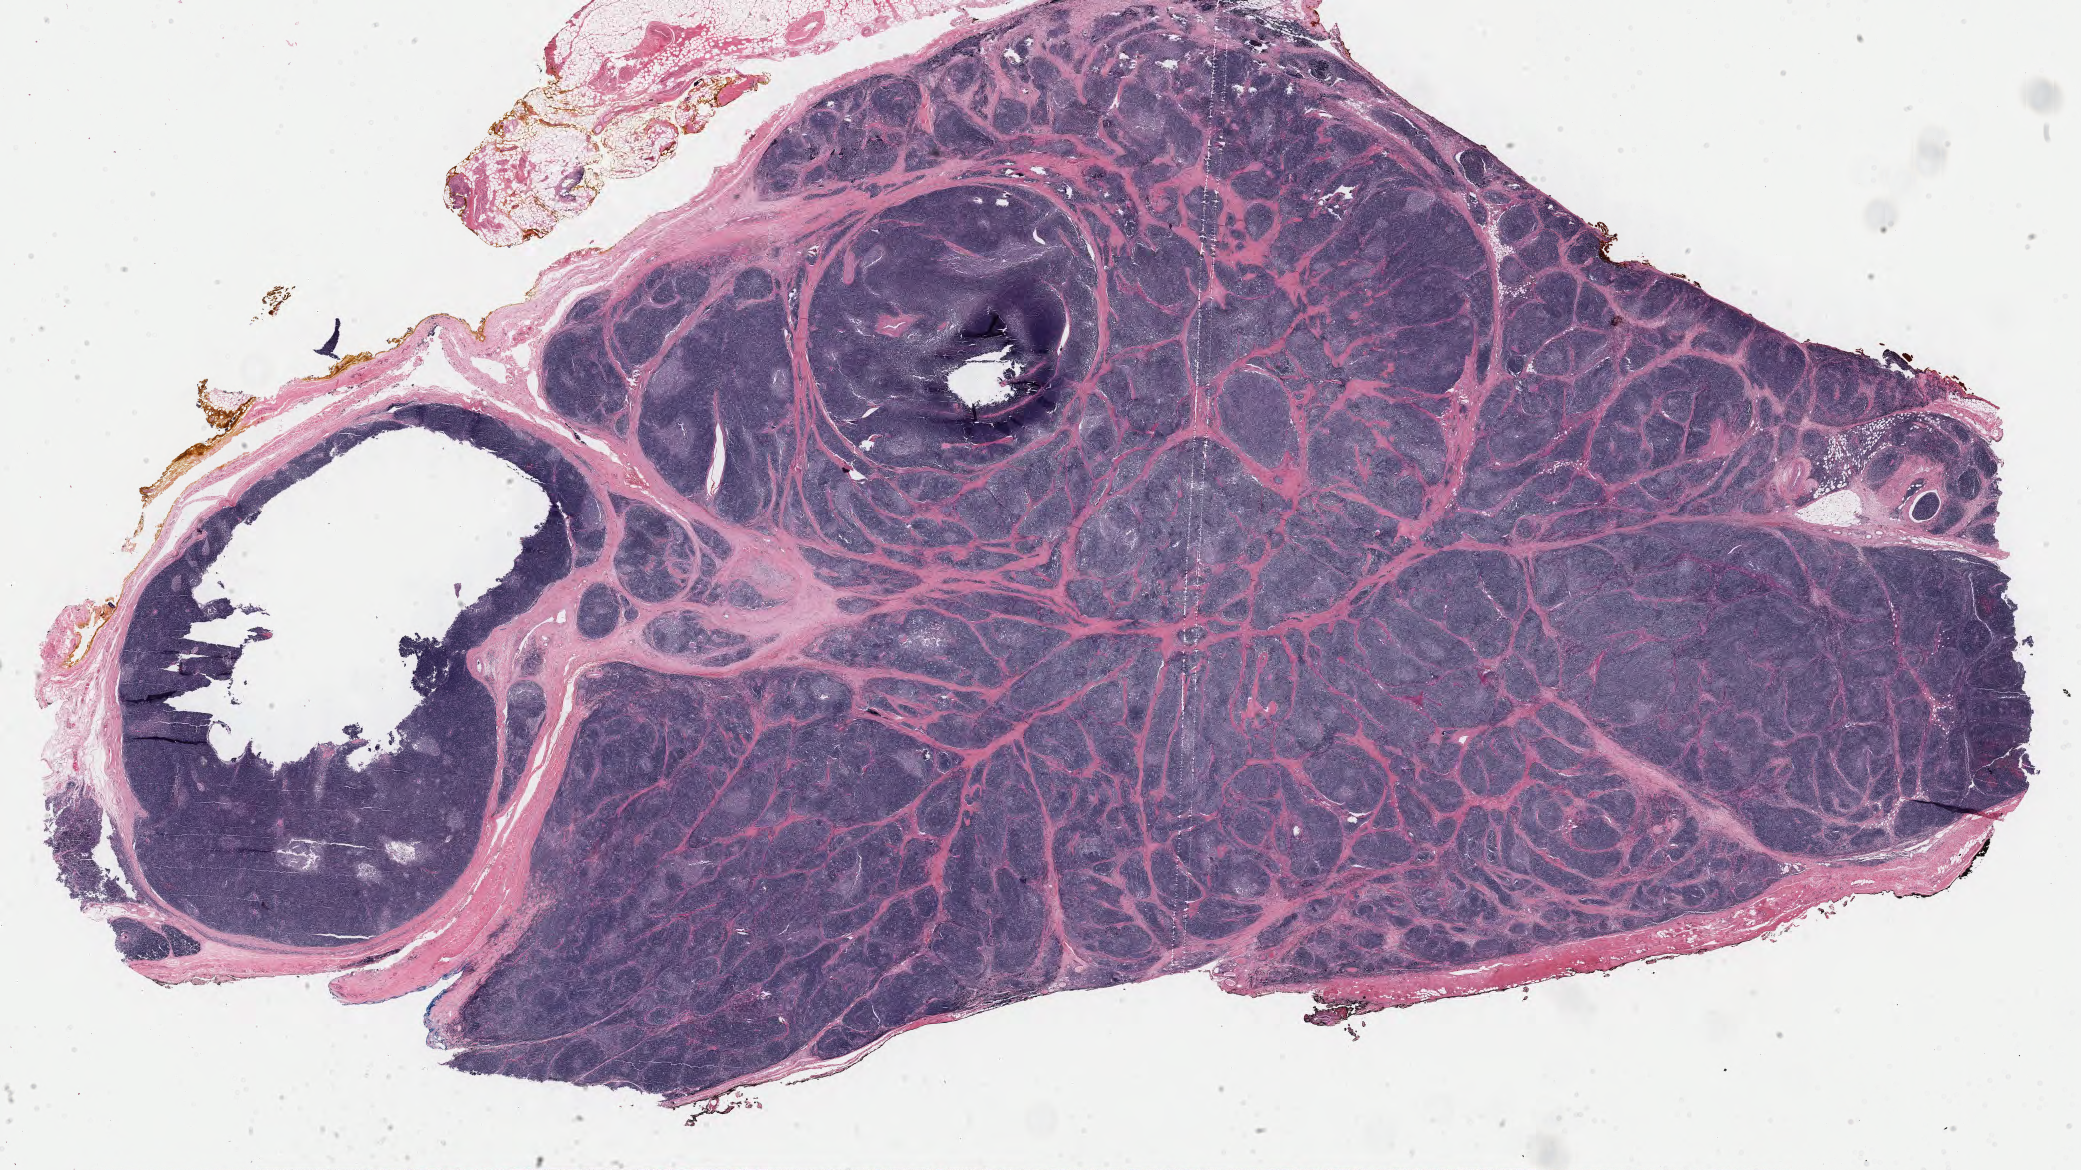
Whole-slide histology image, Hematoxylin and eosin (H&E) stained, a low-resolution overview of the entire scanned area, about 33.0 x 18.5 mm (acquisition: 40x scan); formalin-fixed paraffin-embedded (FFPE) diagnostic section; primary tumour sample from the thymus. Female, age 57 years at initial diagnosis.
• pathologic diagnosis: Thymoma, type B1, NOS